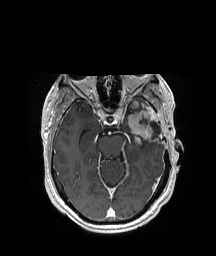
Brain MRI from a brain-tumour surgery series, one axial slice. Position 127 of 208 along the scan axis. T1-weighted post-contrast. 1 mm slice thickness. 216 × 256 image matrix. From the clinical record (not read from this slice): histopathology: Glioblastoma; WHO grade: 4; IDH mutation: no; tumour location: Left Anterior/Superior Temporal.
Structures marked on this image (manually delineated by an expert):
- previous resection cavity: box from (x=139, y=118) to (x=160, y=135) px
- tumour: (x=127, y=99)–(x=157, y=144)